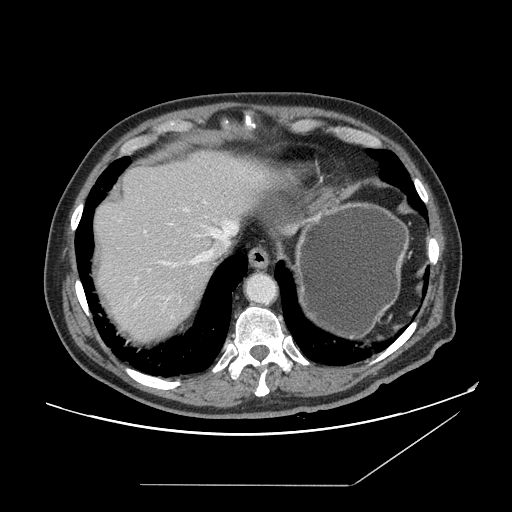
Contrast-enhanced abdominal CT, one axial slice. Slice 130 of 166 in the series (ordered by position). 120 kVp. Soft-tissue window (W 400 / L 40 HU). 512 × 512 image matrix, field of view 416 × 416 mm. Male patient, age 80 years. From the clinical record (not read from this slice): diagnosis: colorectal cancer liver metastases, imaged before liver resection; multiple liver metastases: no; largest metastasis: 2.2 cm.
Structures marked on this image (manually delineated by an expert):
- hepatic veins: bounding box <161,219,237,267> (left, top, right, bottom; pixels)
- liver: <93,148,271,342>
- planned liver remnant (the part of the liver to remain after resection): <93,149,272,257>
- portal vein (with intrahepatic branches): <145,209,190,233>